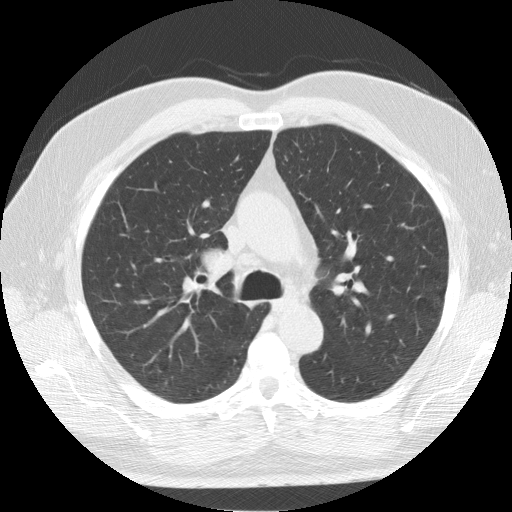
Low-dose screening chest CT, one axial slice; position 96 of 139 along the scan axis; lung window (W 1500 / L -600 HU); 512 × 512 image matrix.
Outlined on this slice (manually delineated by an expert):
- lesion 1 (tumor, upper lobe of right lung): box from (x=203, y=250) to (x=234, y=276) px